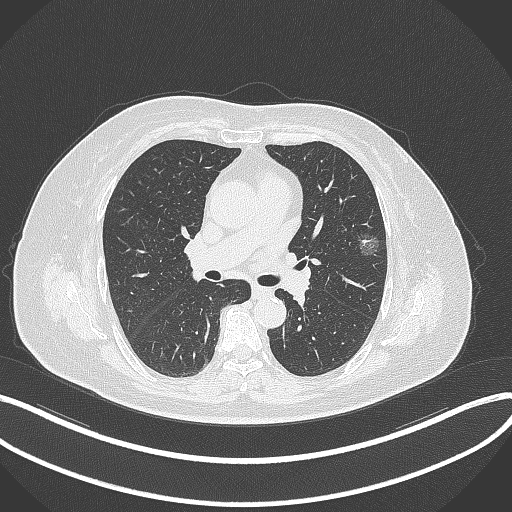
Chest CT, one axial slice; slice 208 of 315 in the series (ordered by position); reconstruction kernel B70f; lung window (W 1500 / L -600 HU); 1 mm slice thickness; 512 × 512 image matrix, field of view 400 × 400 mm. Female patient, age 76 years. From the clinical record (not read from this slice): clinical TNM (as recorded): T1b N0 M0; histopathological grade: G1-2.
Structures marked on this image (rectangle marked by the reading radiologist):
- lung tumour (recorded histology: adenocarcinoma): bounding box (x1, y1, x2, y2) in pixels: (354, 230, 381, 261)